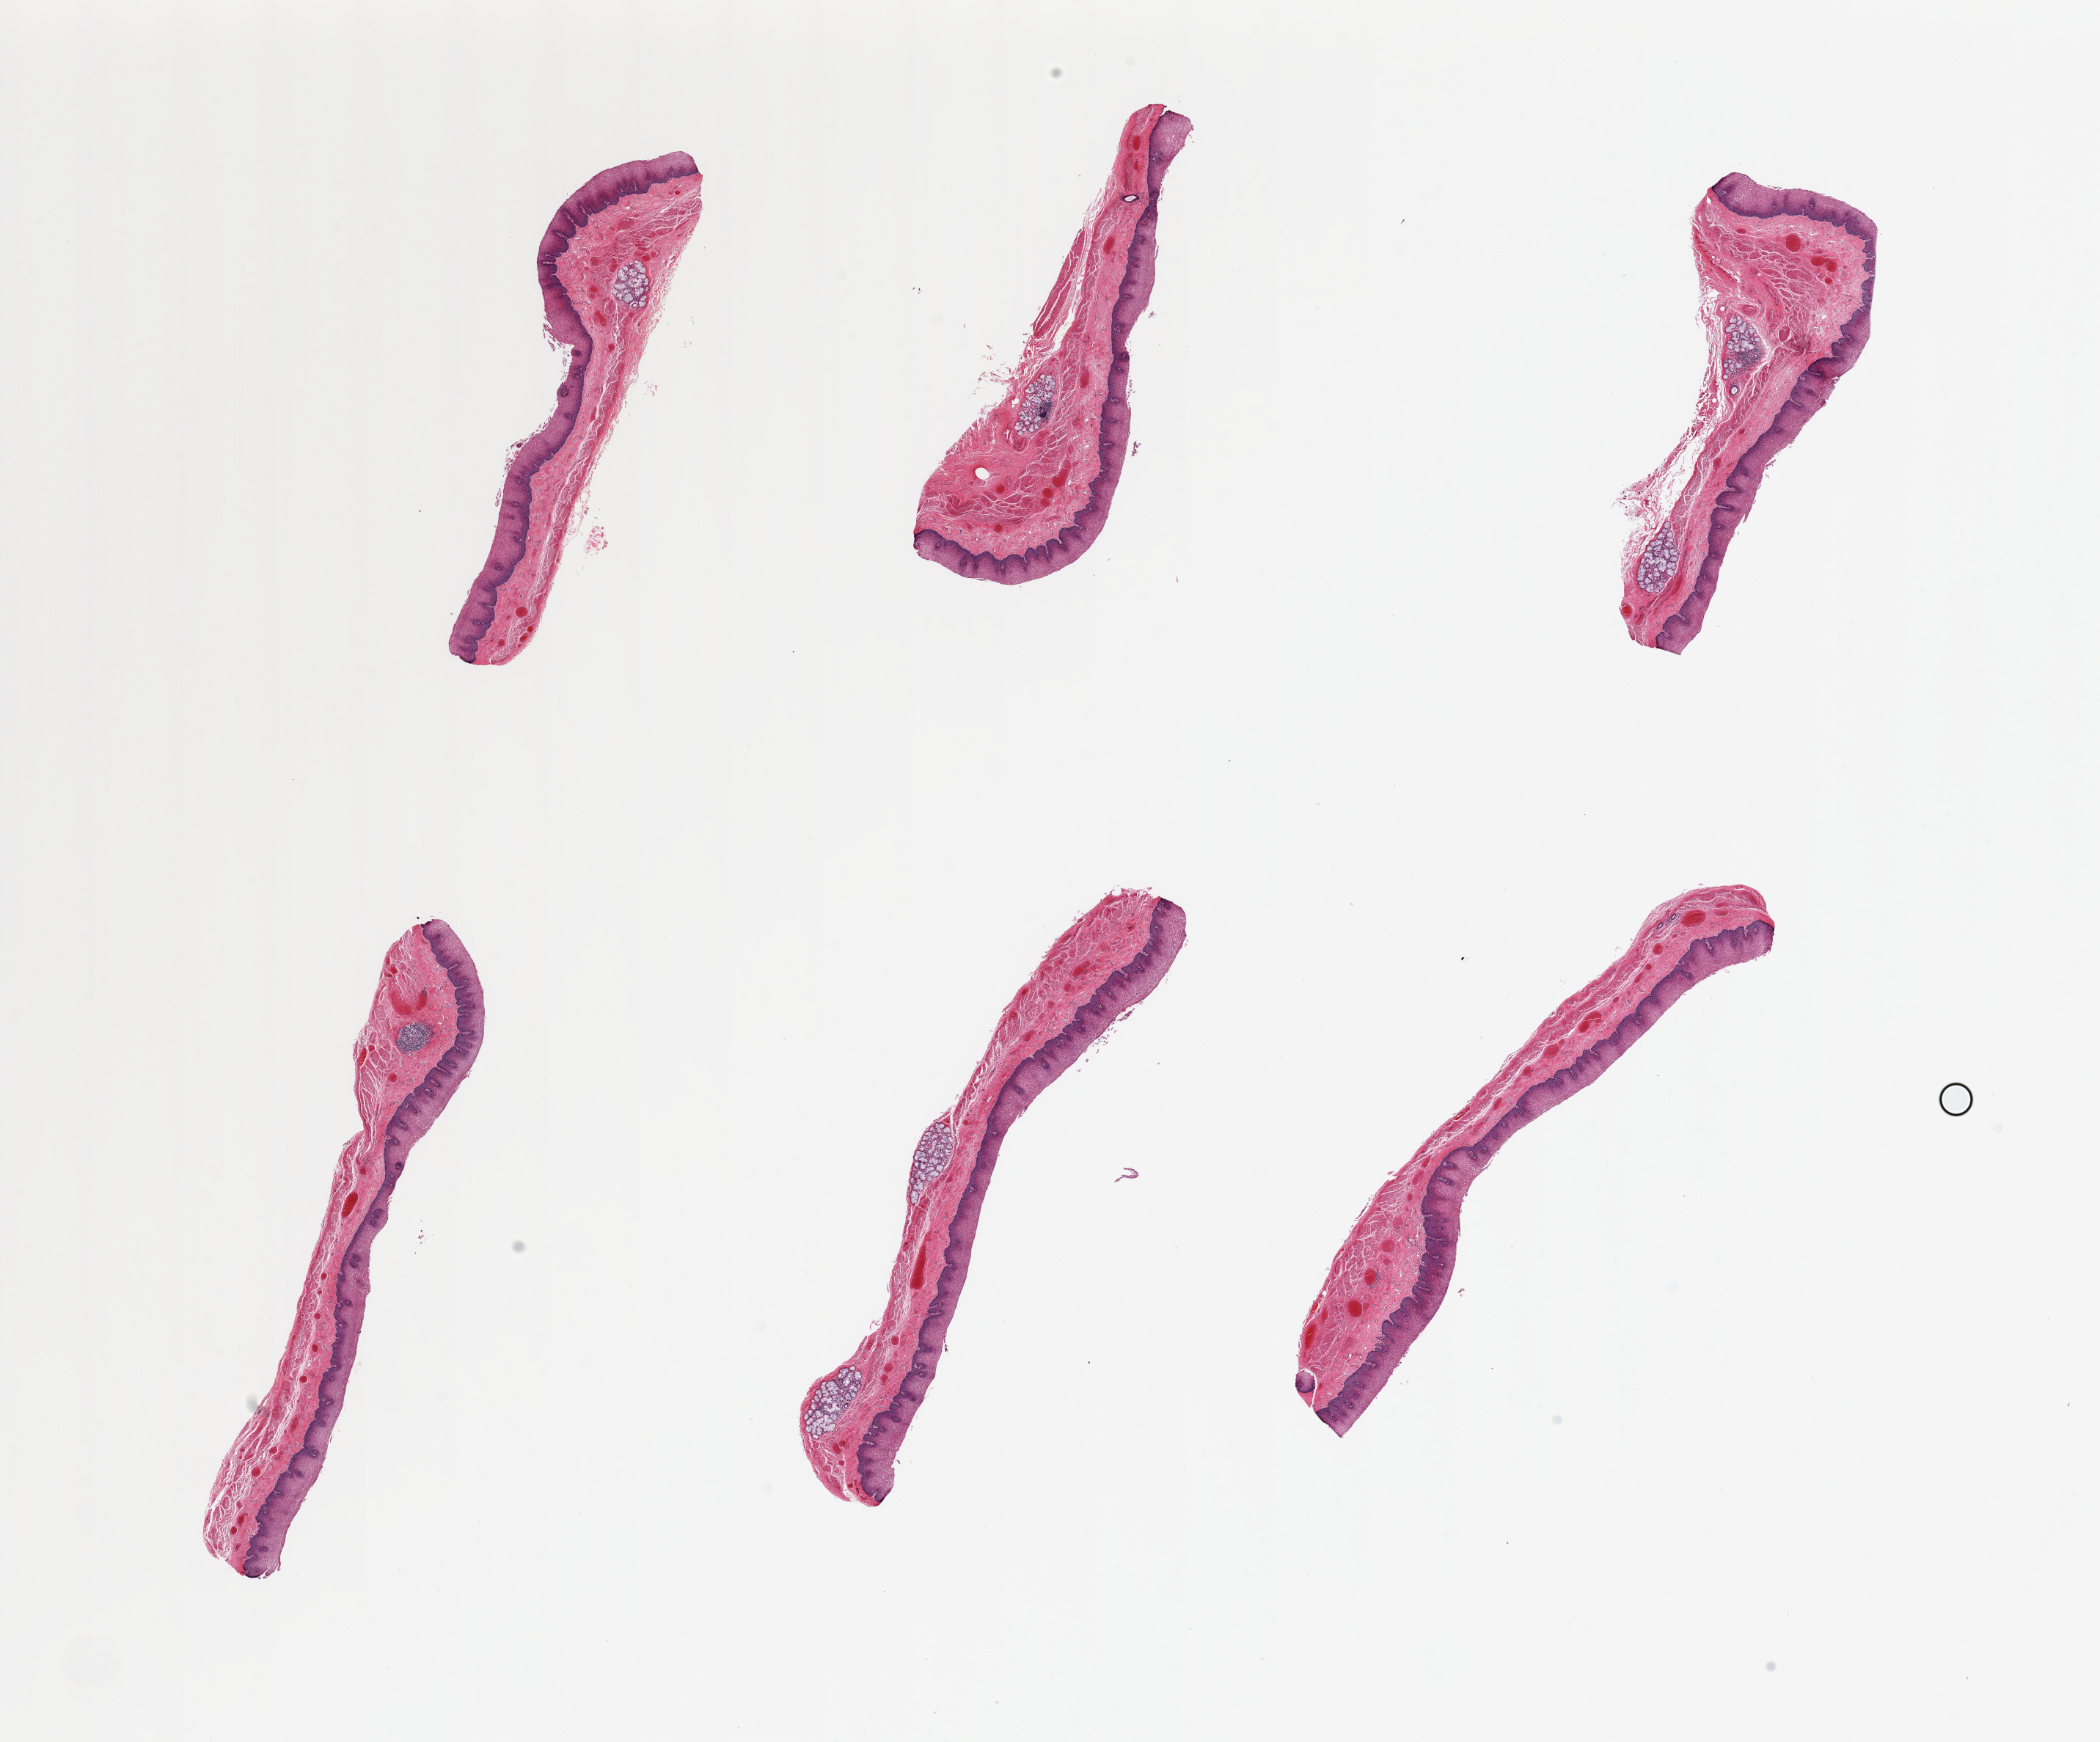
Hematoxylin and eosin (H&E) whole-slide image — a low-resolution overview of the entire scanned area, about 22.6 x 18.8 mm (from a 20x scan), PAXgene-fixed, paraffin-embedded tissue, sampled site (target tissue): esophageal mucous membrane, tissue donor sample. Donor: male.
• reviewer comment on this tissue sample: 6 pieces, squamous mucosa up to ~0.4mm, ~20% thickness; Submucosa mucus glands noted